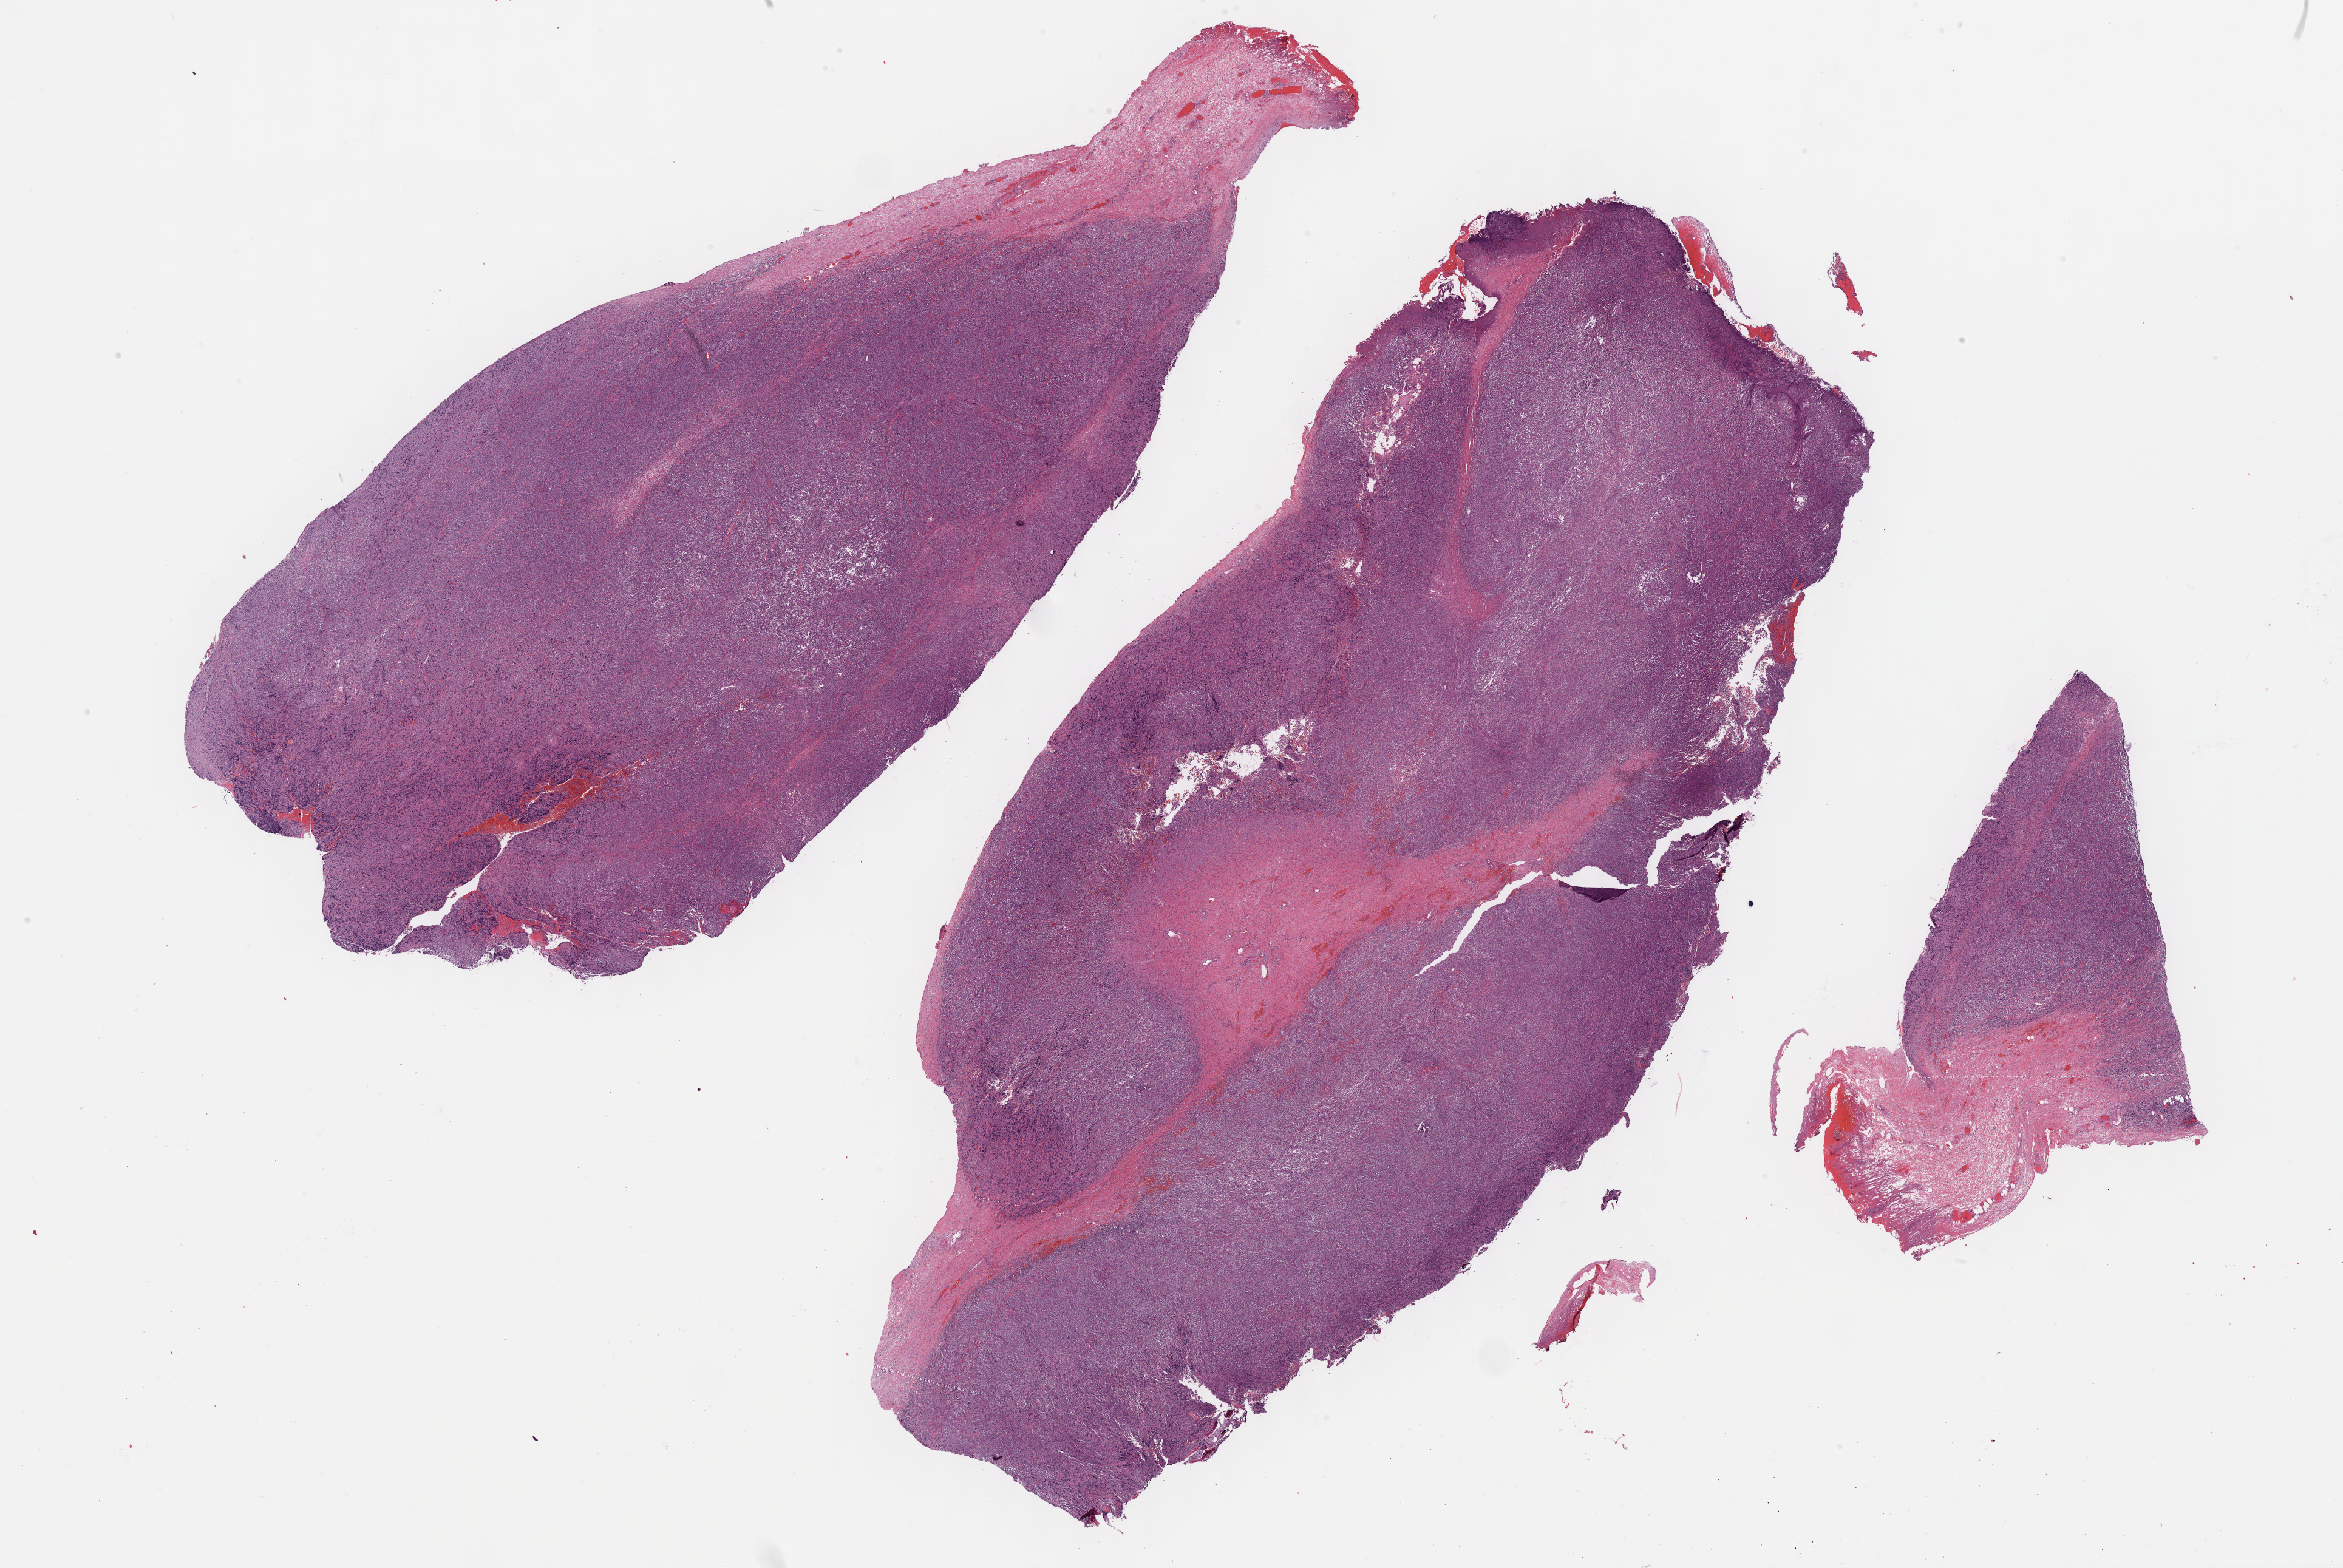
H&E-stained whole-slide image — low-resolution overview of the scanned area, about 31.2 x 20.9 mm. Formalin-fixed paraffin-embedded (FFPE) diagnostic section. Sample: primary tumour, lymphoid tissue. Female patient; age at initial diagnosis 62 years.
- diagnosis: Primary diffuse large B-cell lymphoma of the CNS (bones of skull and face and associated joints)